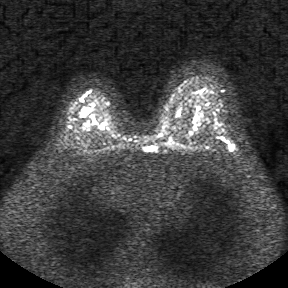
Breast MRI, one axial slice; diffusion-weighted series; image 2 of 4 stored at this slice position (different b-values; order by instance number); 1.5 T; 5 mm slice thickness; 288 × 288 image matrix, field of view 340 × 340 mm. Female patient.
Structures marked on this image (manually delineated by an expert):
- tumour on diffusion-weighted imaging: box from (x=80, y=109) to (x=88, y=116) px